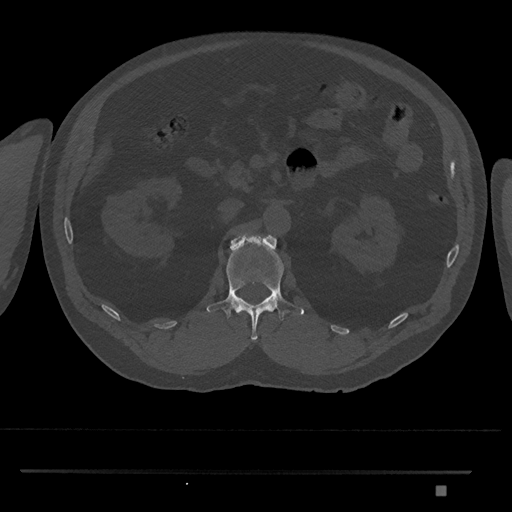
CT including the spine, one axial slice. Reconstruction kernel Br40s/3. 120 kVp. Bone window (W 1800 / L 400 HU). 512 × 512 image matrix. Male patient, age 65 years. Case-level facts recorded for this patient, not image findings: primary cancer: prostate.
Outlined on this slice (semi-automatically segmented with operator editing):
- L1 vertebra: bounding box <207,233,304,341> (left, top, right, bottom; pixels)